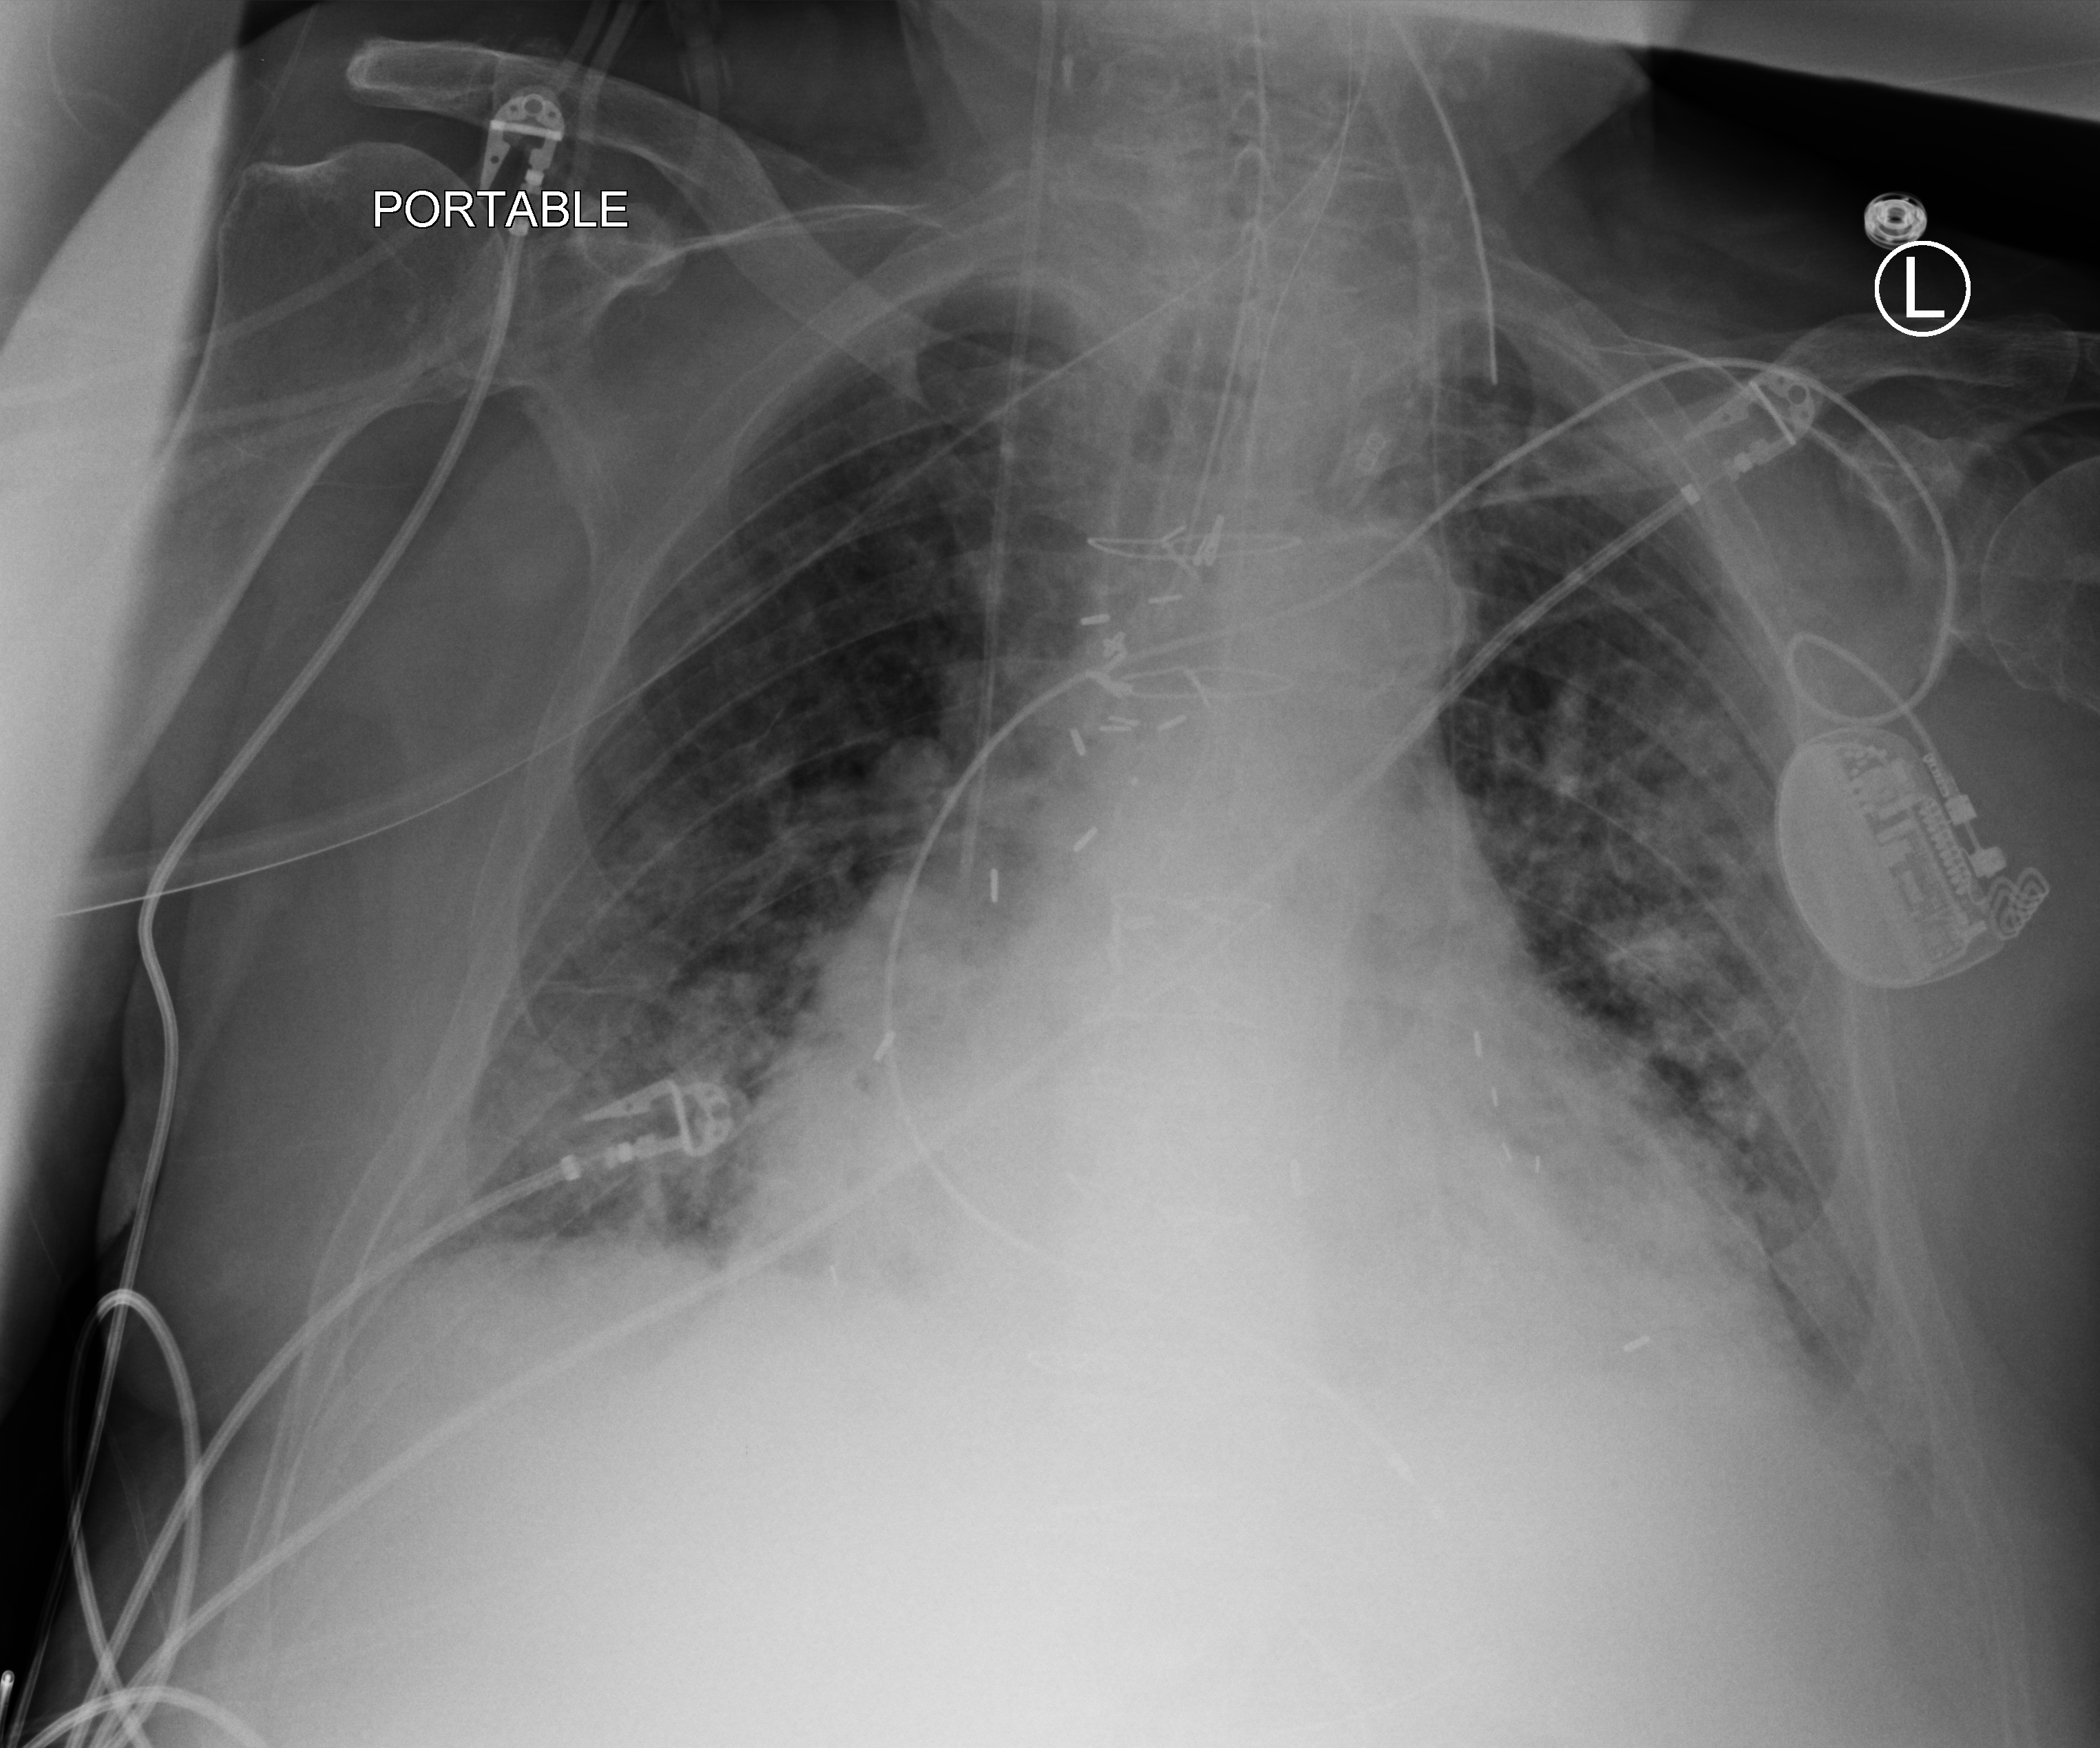
Portable chest radiograph; anteroposterior (AP) projection. Male patient hospitalised with COVID-19, age 75–90 years.
Hospital-stay facts (about this admission, not read from this image; timing relative to this image not recorded): length of hospital stay: 16 days; admitted to intensive care during this hospital stay: yes.